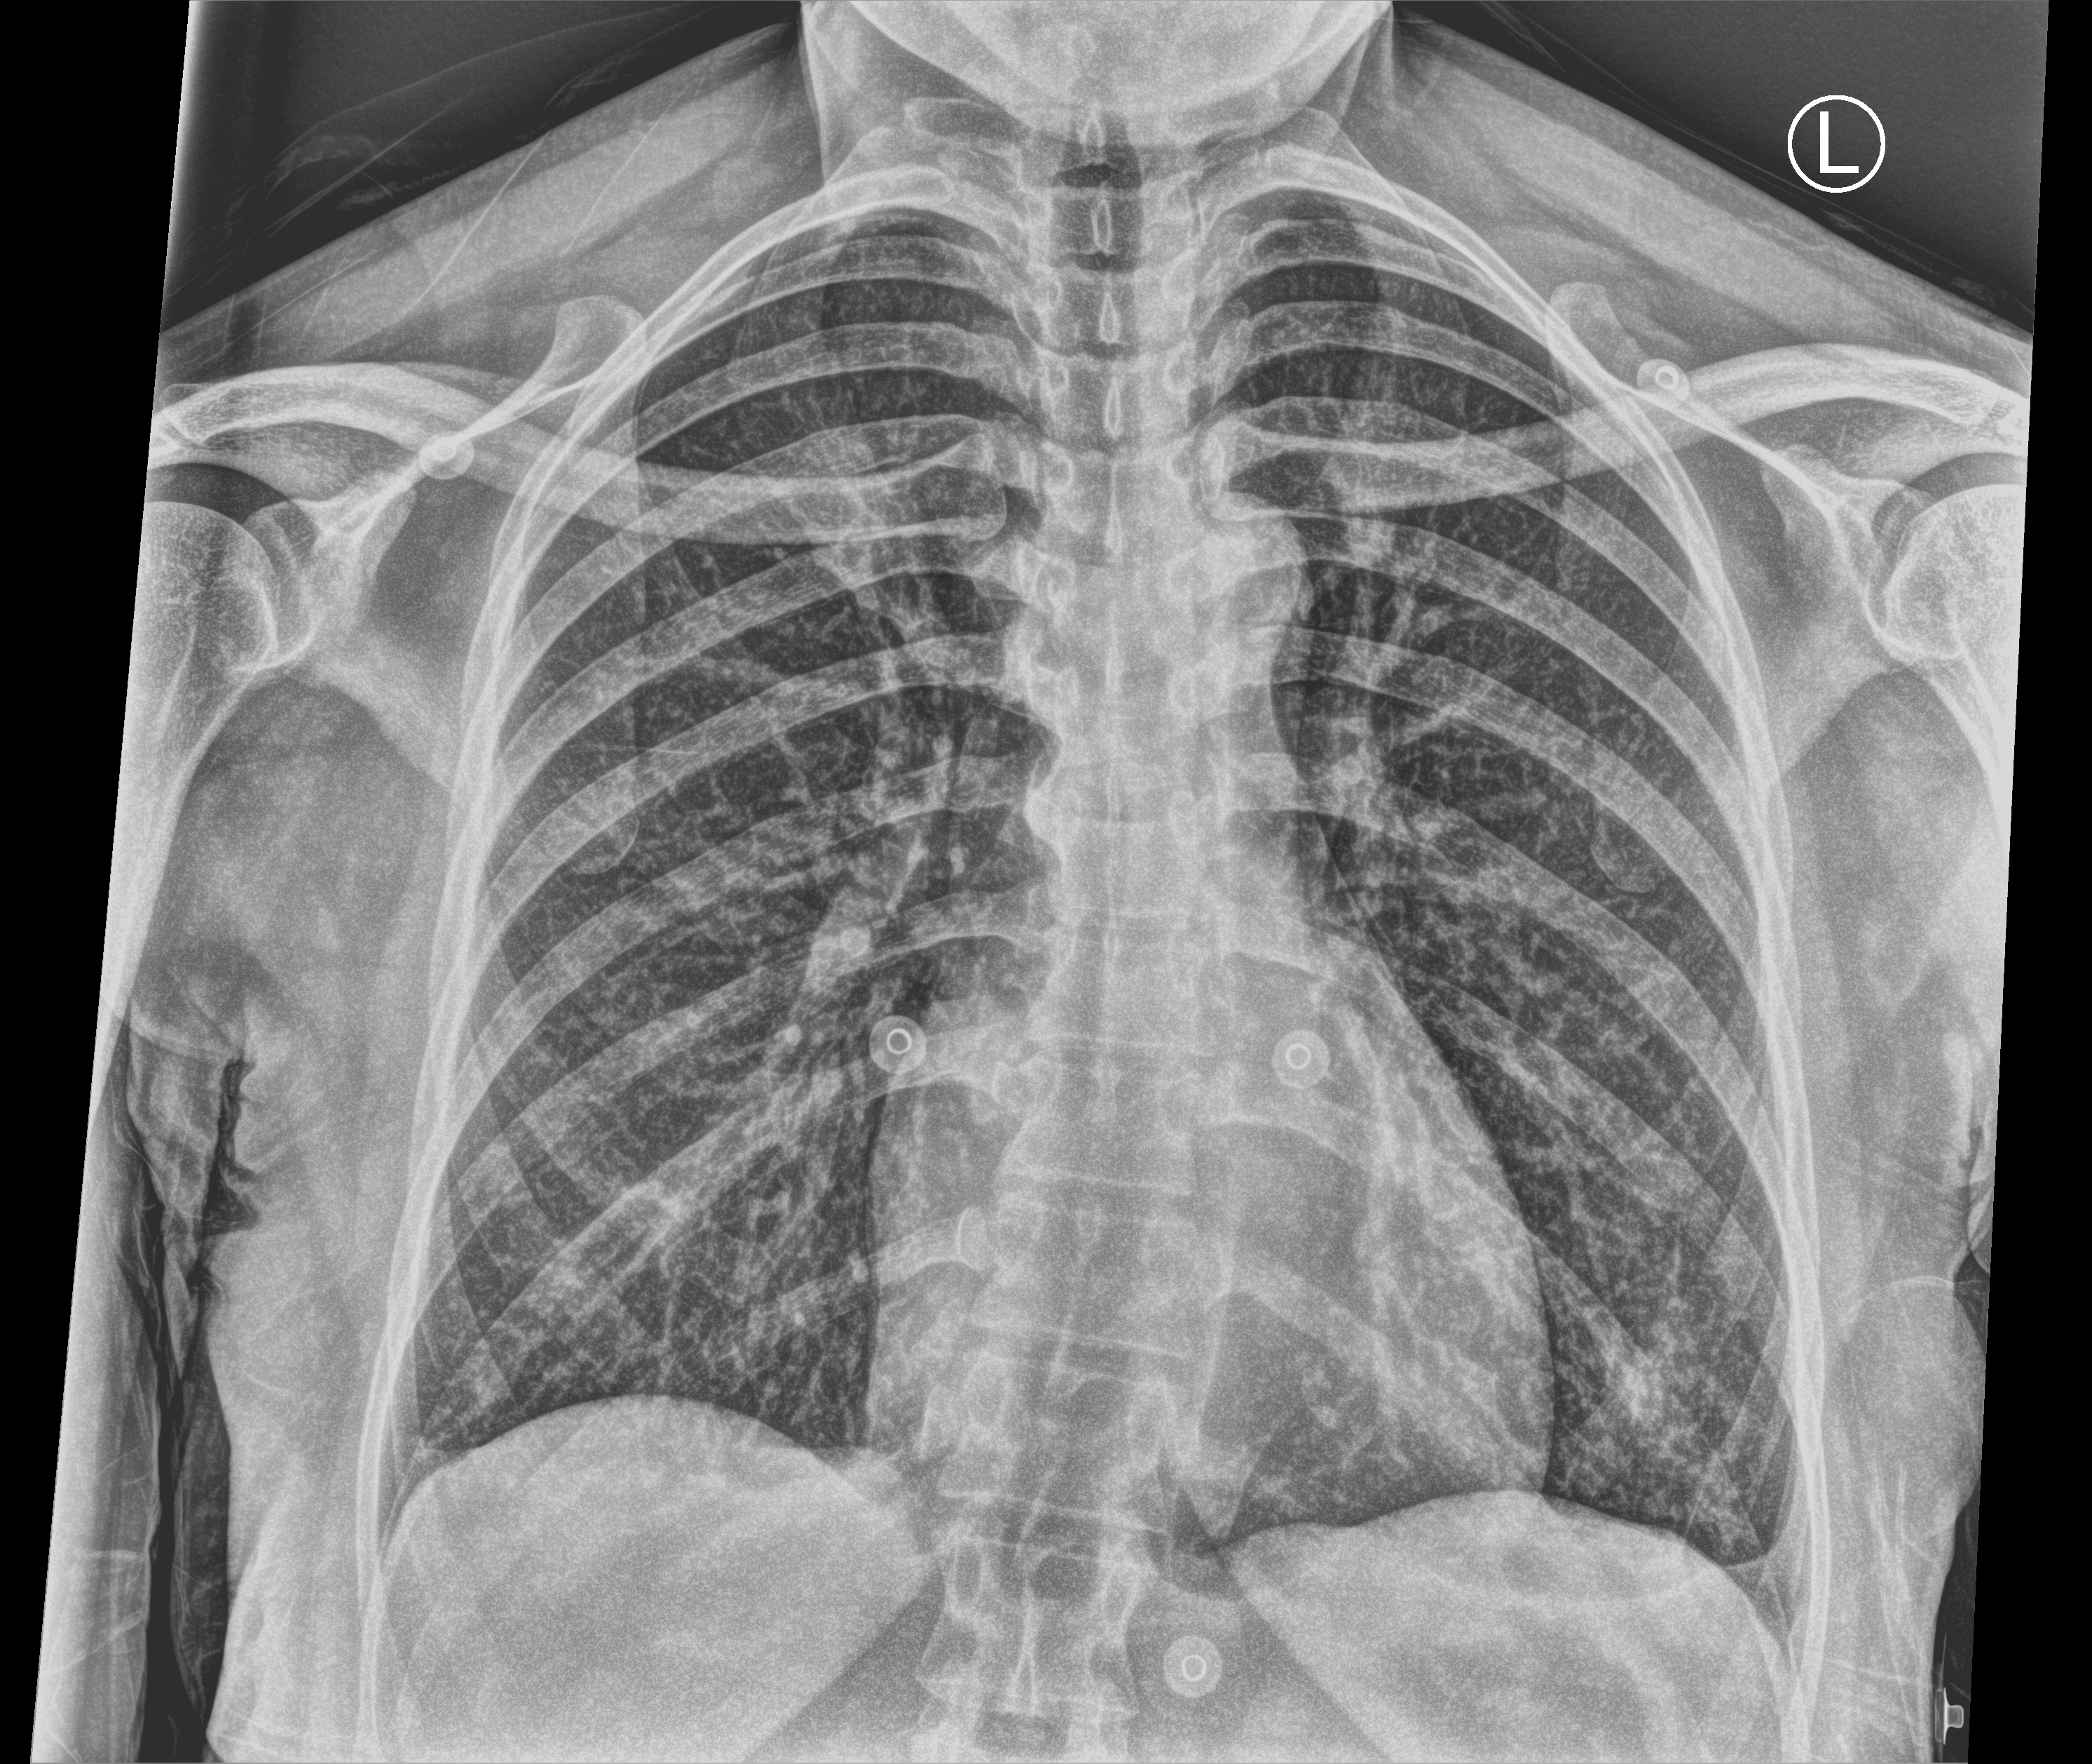
Chest X-ray (portable), anteroposterior (AP) projection. Patient hospitalised with COVID-19; female, aged 18–59 years.
From the hospital-stay record, not from the radiograph (when in the stay this image was taken is not recorded): hypertension (admission record): yes.